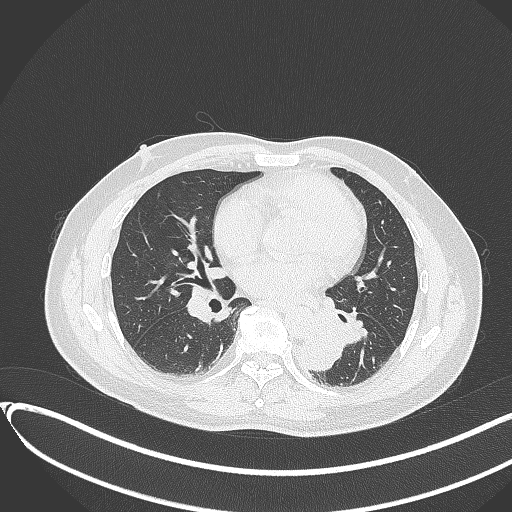
Chest CT, one axial slice; slice 157 of 417 in the series (ordered by position); reconstruction kernel B70f; 120 kVp; lung window (W 1500 / L -600 HU); 512 × 512 image matrix, field of view 400 × 400 mm. Male patient, age 54 years. From the clinical record (not read from this slice): clinical TNM (as recorded): T3 N0 M0.
Outlined on this slice (rectangle marked by the reading radiologist):
- lung tumour (recorded histology: squamous cell carcinoma): box from (x=300, y=328) to (x=348, y=375) px